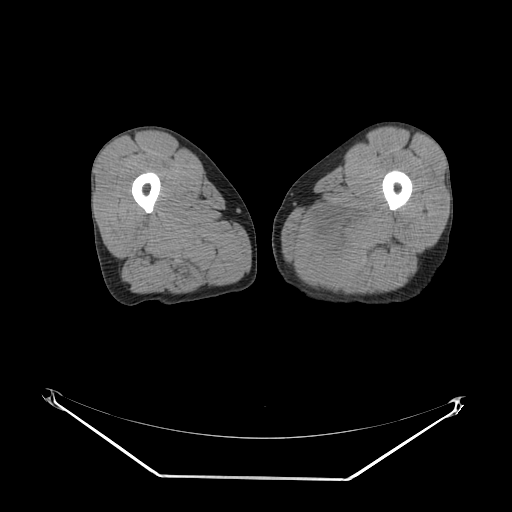
CT of an extremity soft-tissue mass (from a PET/CT study), one axial slice; position 13 of 267 along the scan axis; 140 kVp; soft-tissue window (W 400 / L 40 HU); 512 × 512 image matrix. Male patient. From the clinical record (not read from this slice): histological type: pleiomorphic liposarcoma; grade: high; site of the primary tumour: left thigh.
Annotated regions visible in this slice (expert contour drawn on MRI and transferred to this co-registered scan by the dataset authors):
- gross tumour volume including surrounding oedema: box from (x=313, y=203) to (x=375, y=273) px
- gross tumour volume (mass): (x=335, y=253)–(x=339, y=255)